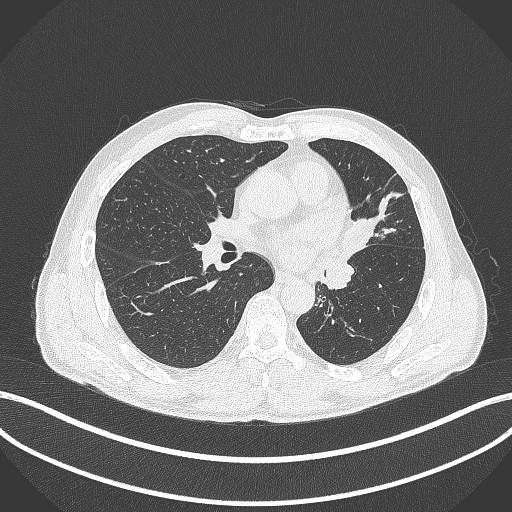
Chest CT, one axial slice. Position 221 of 429 along the scan axis. Reconstruction kernel B70f. Lung window (W 1500 / L -600 HU). 1 mm slice thickness. 512 × 512 image matrix, field of view 400 × 400 mm. Patient: male, 57 years. From the clinical record (not read from this slice): clinical TNM (as recorded): T2b N0 M0.
Annotated regions visible in this slice (rectangle marked by the reading radiologist):
- lung tumour (recorded histology: squamous cell carcinoma): bounding box [x1, y1, x2, y2] px = [339, 203, 378, 264]